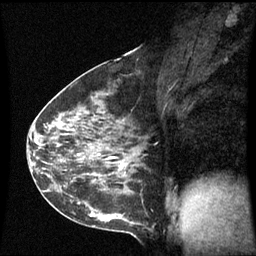
Breast MRI (dynamic contrast-enhanced), one sagittal slice. Position 32 of 60 along the scan axis. Dynamic contrast-enhanced series, image 2 of 3 at this slice position (ordered by acquisition). 1.5 T. TE 4.2 ms, TR 8.9 ms. 256 × 256 image matrix, field of view 210 × 210 mm. Patient: female, 43 years. From the clinical record (not read from this slice): setting: breast cancer imaged before/during neoadjuvant chemotherapy; receptor status: HER2-positive.
Structures marked on this image (semi-automatically segmented with operator editing):
- analysis volume of interest (the breast-tissue region the enhancement analysis was run in; not a lesion): bounding box (x1, y1, x2, y2) in pixels: (56, 80, 143, 195)
- tumour enhancement mask (voxels above the 70 % enhancement threshold inside the analysis volume of interest): (99, 155, 125, 169)